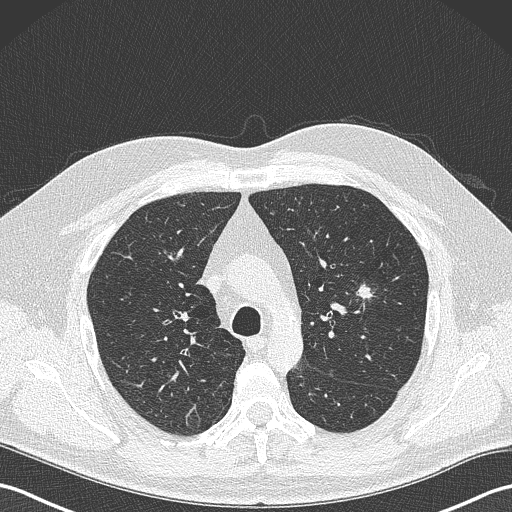
Low-dose screening chest CT, one axial slice; position 242 of 343 along the scan axis; reconstruction kernel B50f; lung window (W 1500 / L -600 HU); 512 × 512 image matrix, field of view 350 × 350 mm.
Structures marked on this image (manually delineated by an expert):
- lesion 1 (tumor, upper lobe of left lung): bounding box <356,284,375,302> (left, top, right, bottom; pixels)